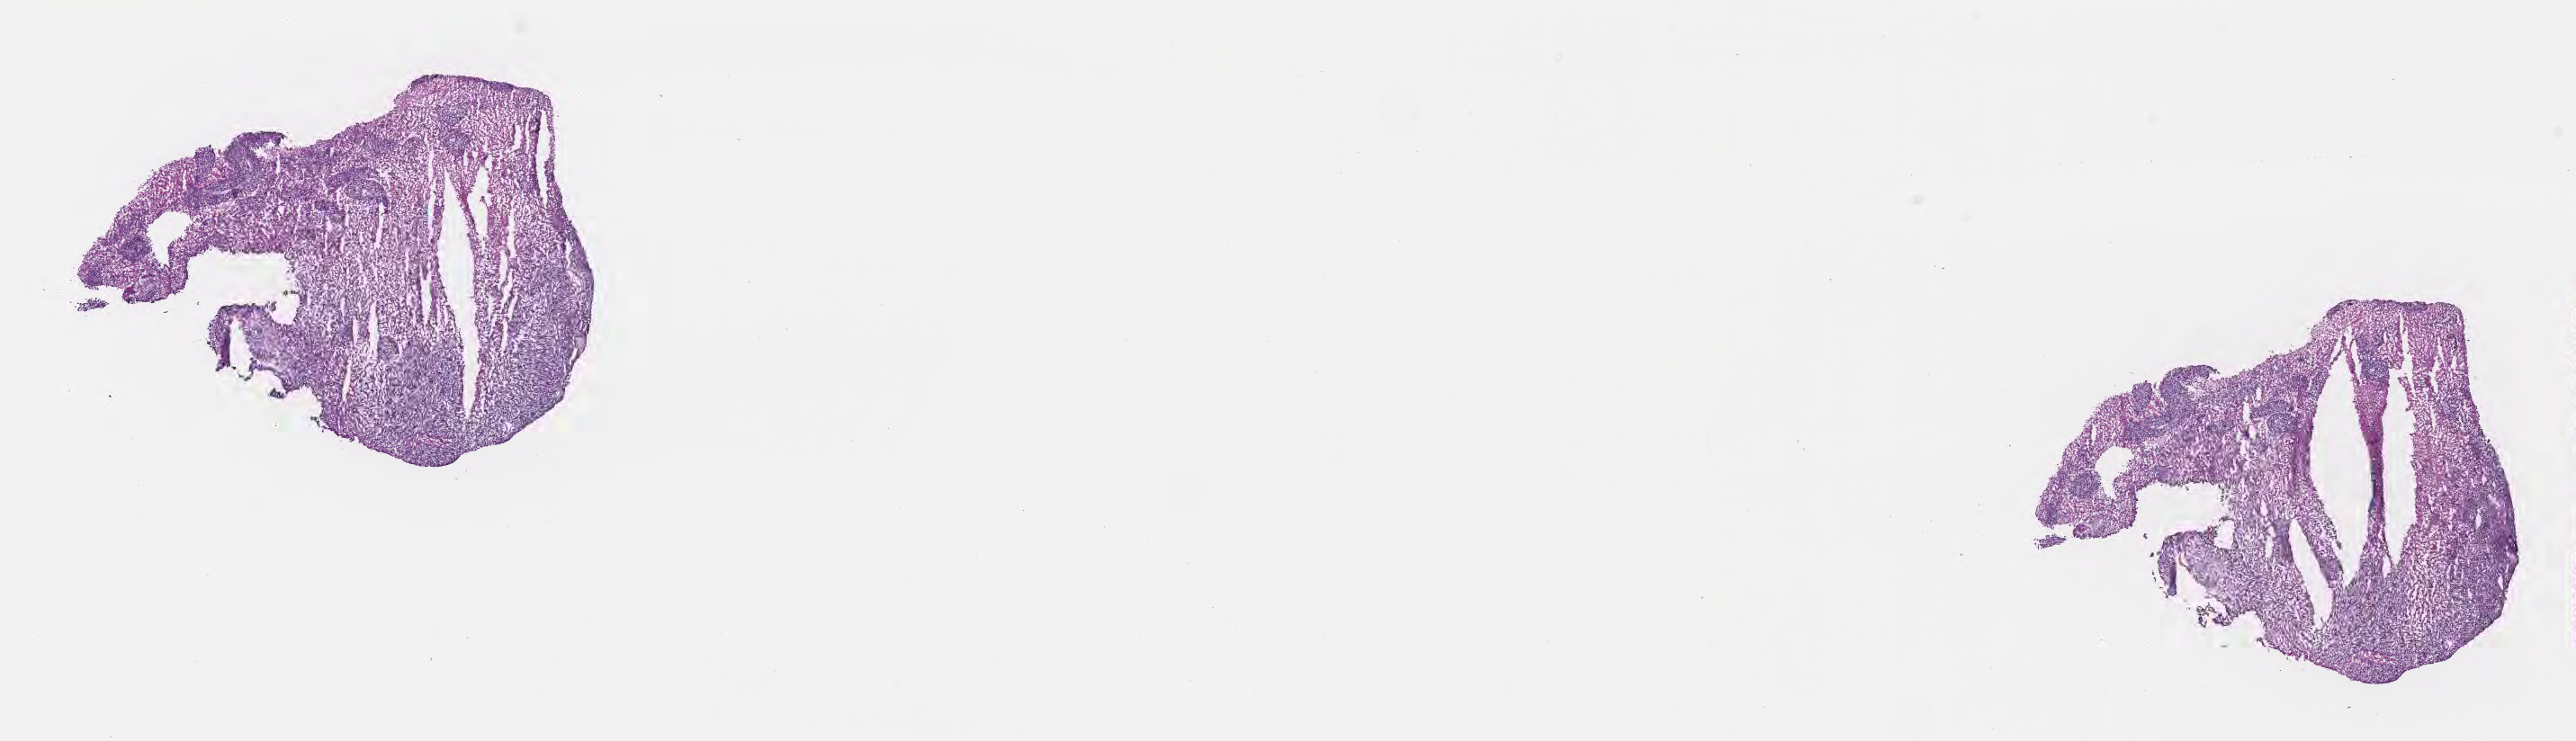
Digitized haematoxylin and eosin-stained section, whole scanned area (about 23.1 x 6.7 mm) shown as a low-resolution overview. Frozen section (tissue freezing medium). Specimen: metastatic tumor tissue, resected from brain. Female patient; age at initial diagnosis 47 years. Slide review estimates, as recorded: tumor cells 70%, tumor nuclei 70%, stromal cells 10%, necrosis 20%, normal cells 0%. Inflammatory infiltration, as recorded: lymphocyte infiltration 4%, monocyte infiltration 1%, neutrophil infiltration 3%.
- patient diagnosis (primary): Malignant melanoma, NOS